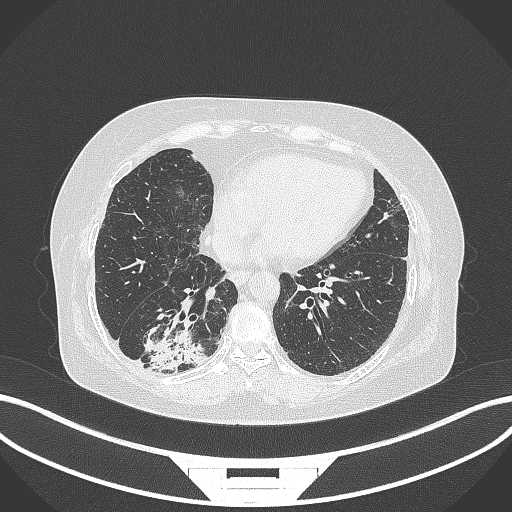
Chest CT, one axial slice. Position 75 of 296 along the scan axis. Reconstruction kernel B70f. Lung window (W 1500 / L -600 HU). 1 mm slice thickness. 512 × 512 image matrix, field of view 400 × 400 mm. Patient: female, 65 years. Case-level facts recorded for this patient, not image findings: clinical TNM (as recorded): T2b N1 M0.
Outlined on this slice (bounding box drawn by a radiologist):
- lung tumour (recorded histology: adenocarcinoma): bounding box [x1, y1, x2, y2] px = [139, 320, 213, 375]